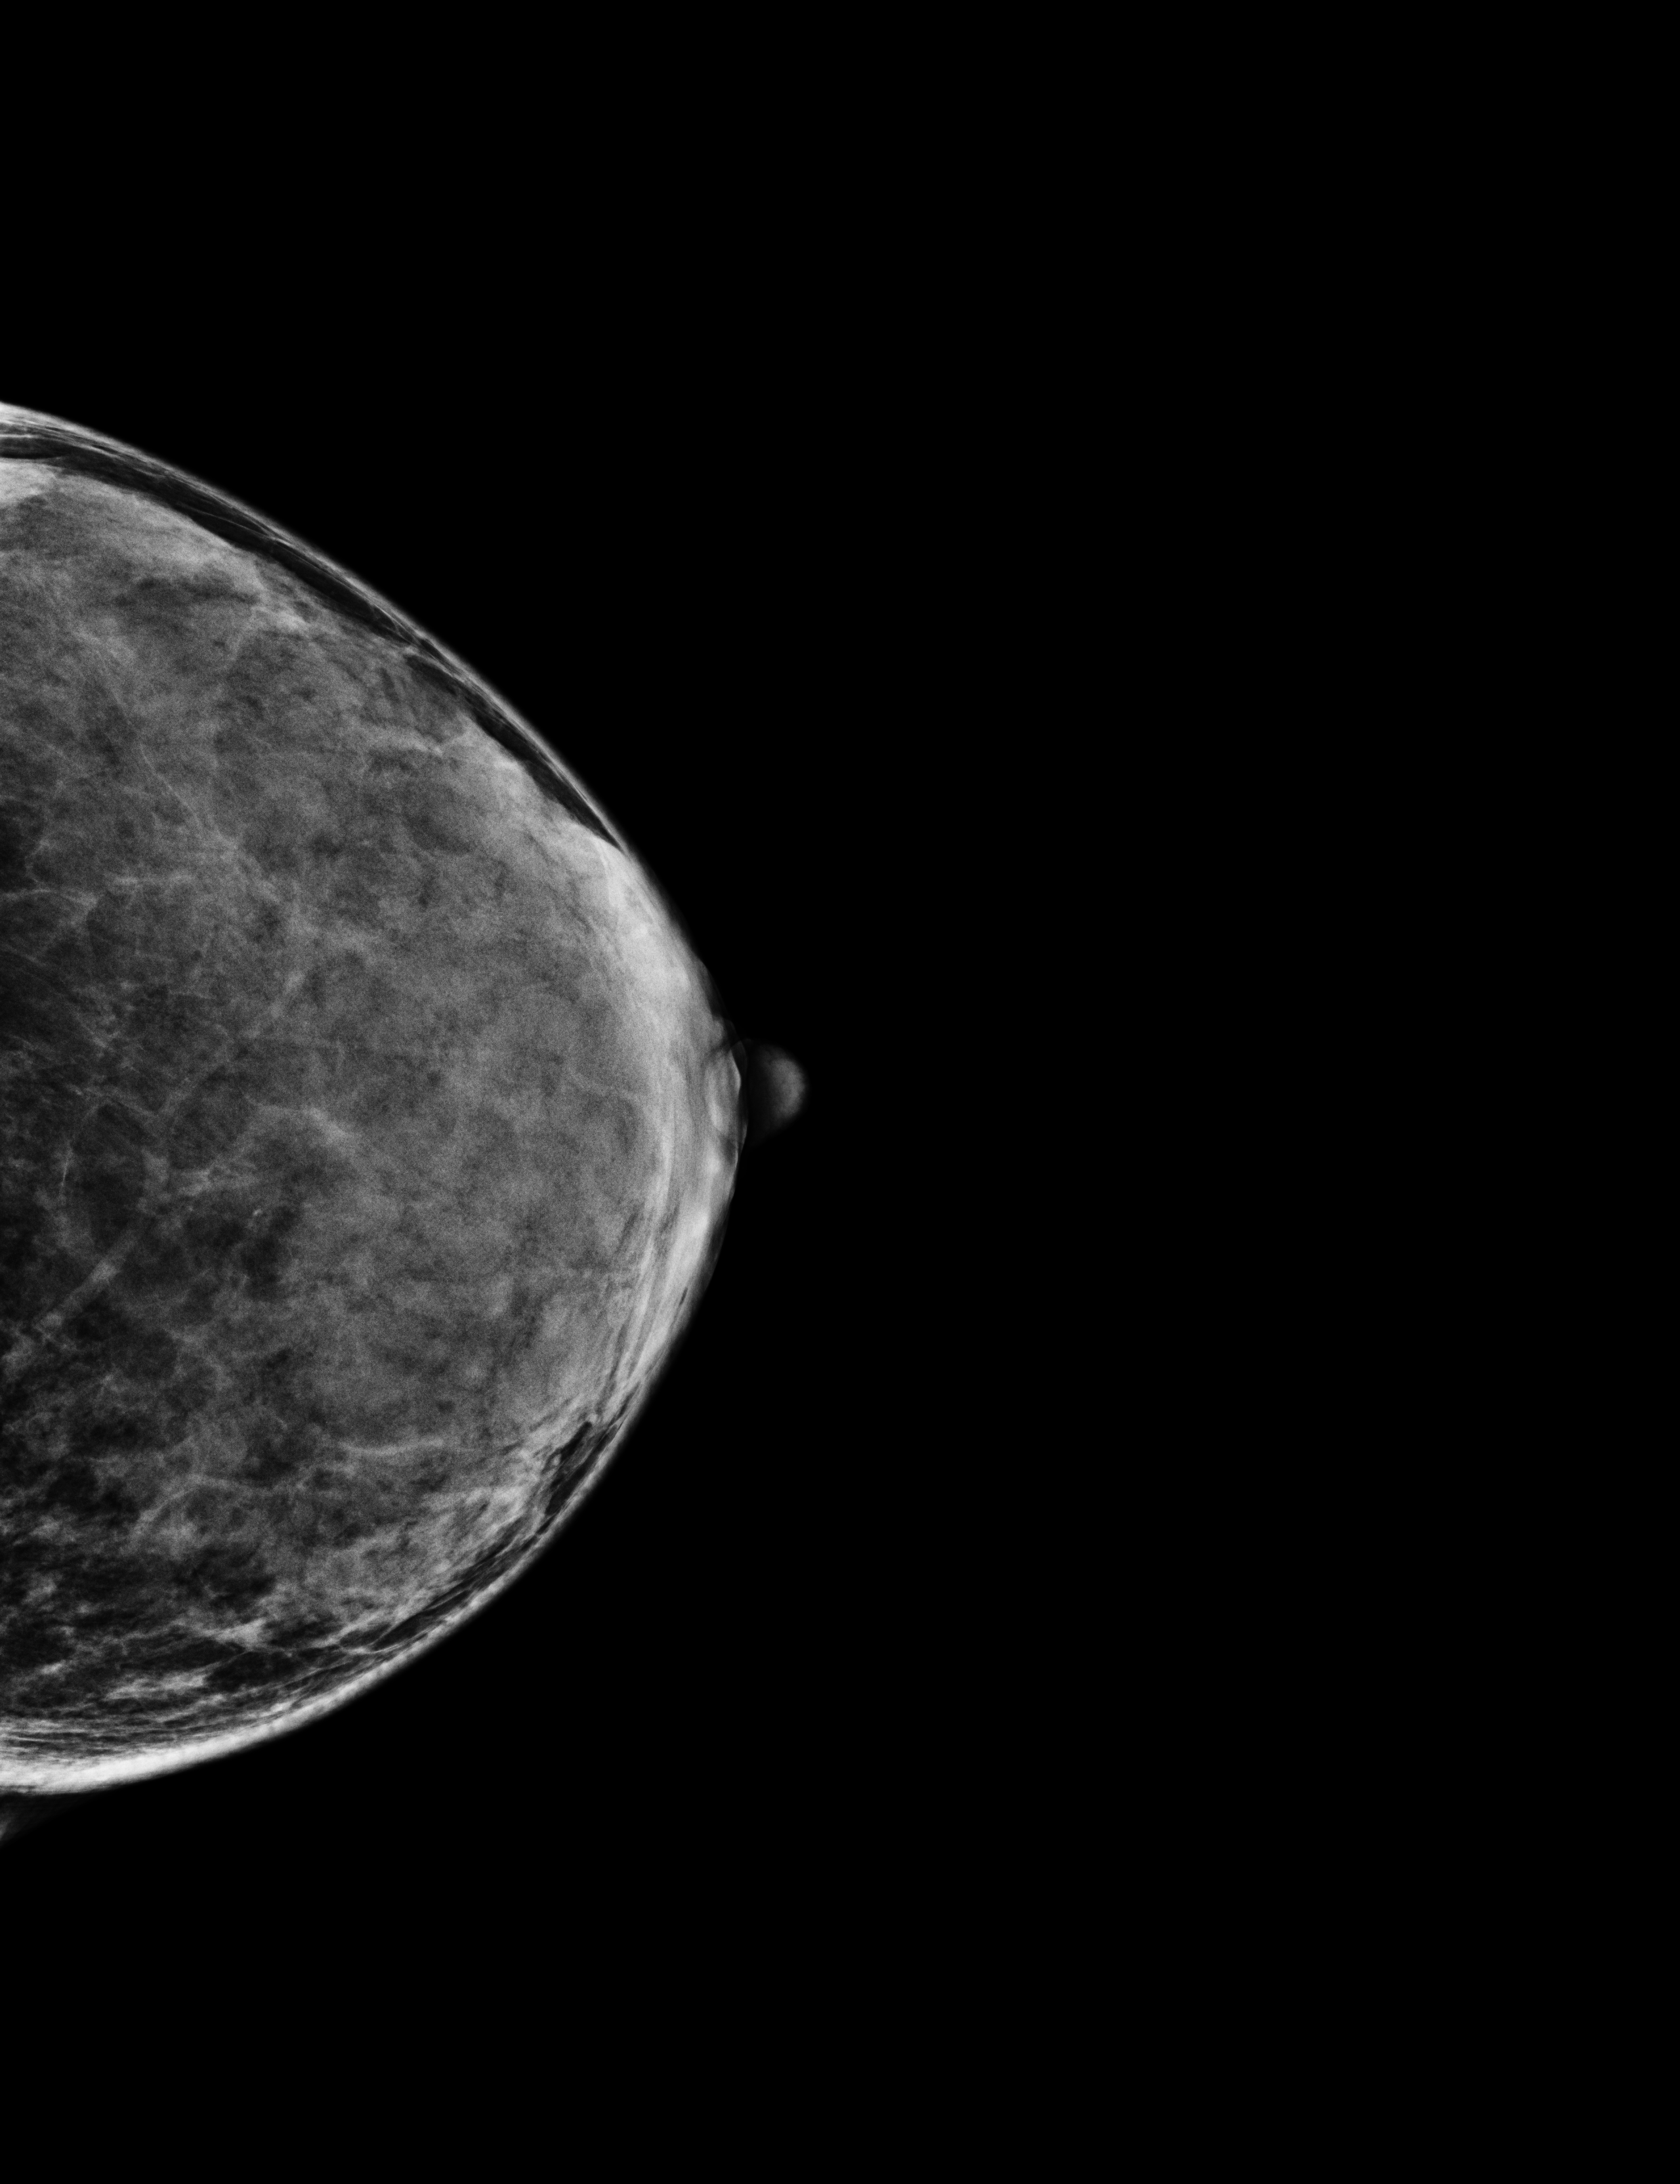
Screening examination; system: Selenia Dimensions.
Image type: full-field digital mammogram. Breast: left. Projection: cranio-caudal projection.